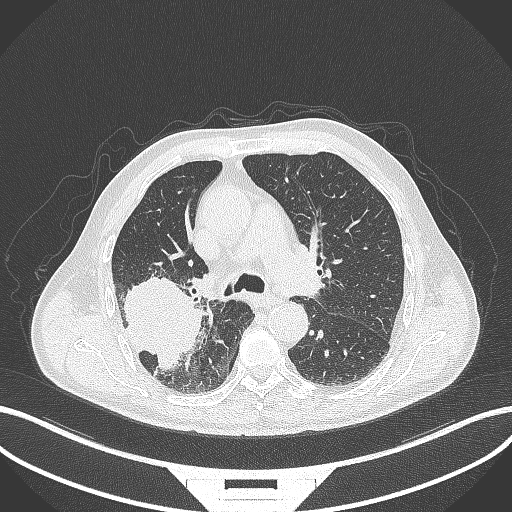
Chest CT, one axial slice; position 261 of 429 along the scan axis; reconstruction kernel B70f; 120 kVp; lung window (W 1500 / L -600 HU); 512 × 512 image matrix. Male patient, age 72 years. From the clinical record (not read from this slice): clinical TNM (as recorded): T3 N2 M0.
Outlined on this slice (rectangle marked by the reading radiologist):
- lung tumour (recorded histology: adenocarcinoma): bounding box <118,271,209,380> (left, top, right, bottom; pixels)